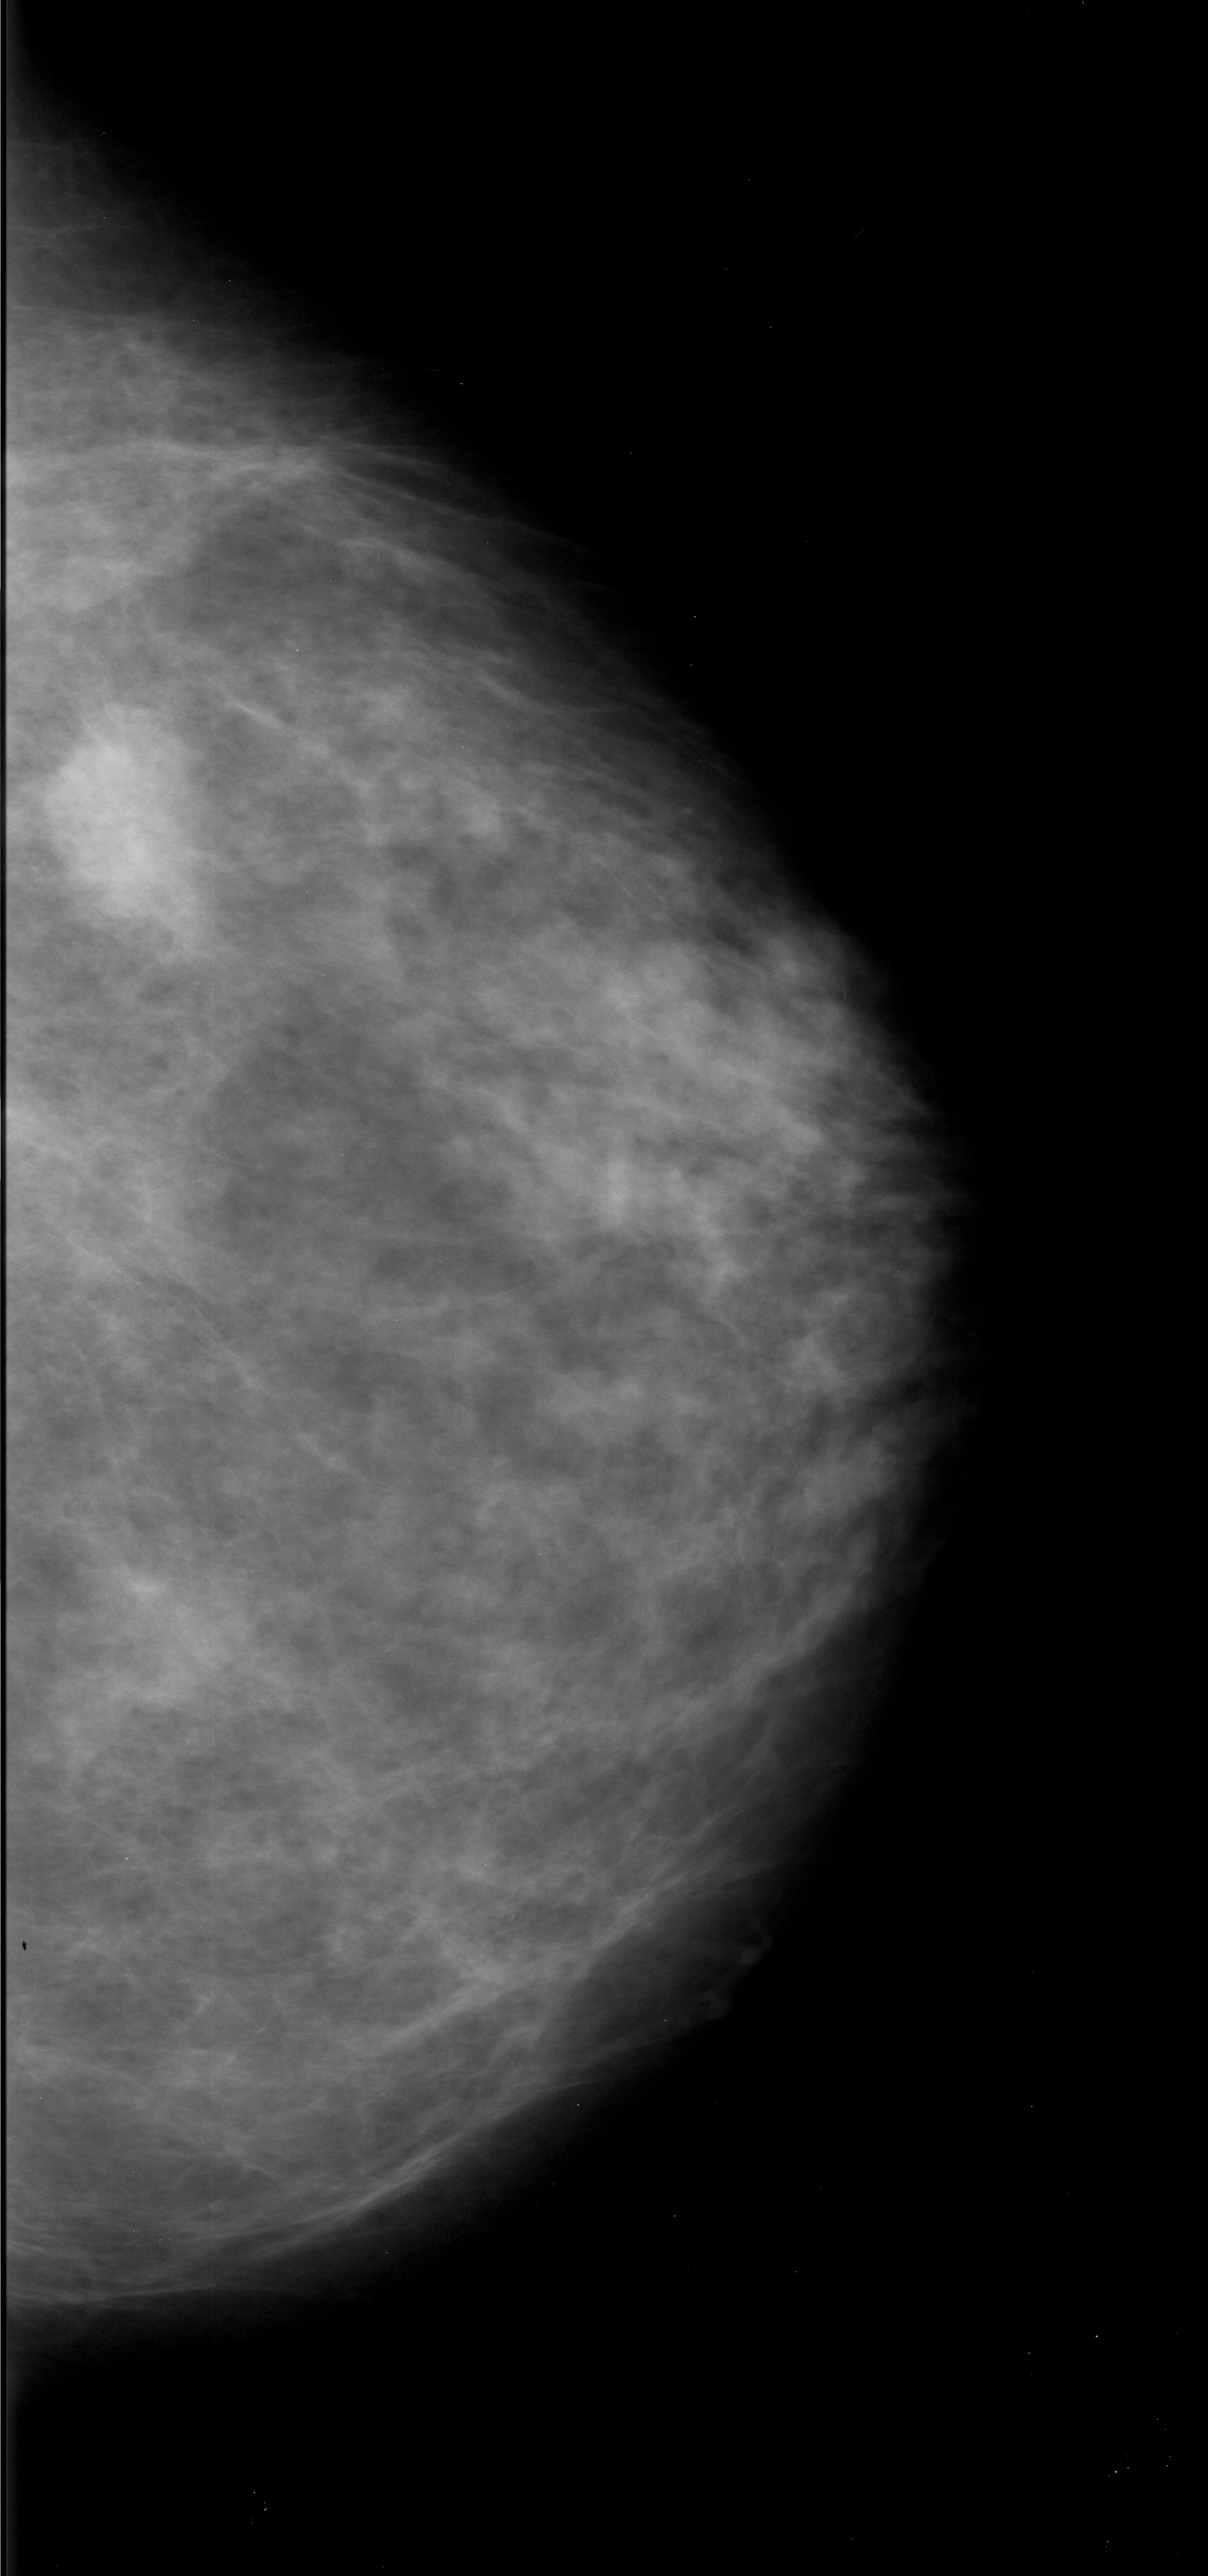
Mammogram (digitized film). Right breast. CC view. 1208 × 2576 image matrix.
Expert-marked regions of interest on this film, with their recorded descriptors:
- mass, shape irregular, margins ill defined; BI-RADS assessment category 4; subtlety rating 4 on a 1 (subtle) to 5 (obvious) scale; pathology (as recorded): malignant: box from (x=35, y=710) to (x=208, y=948) px